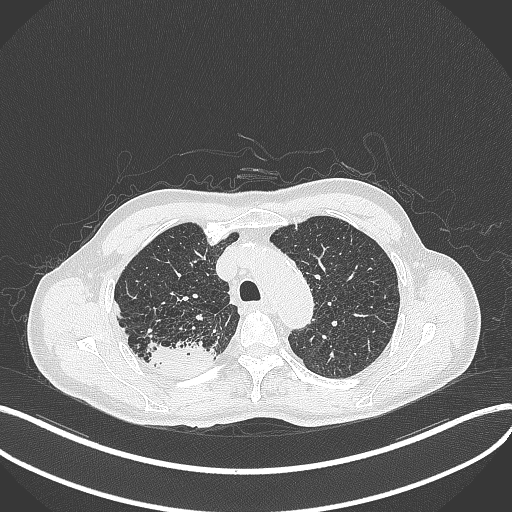
Chest CT, one axial slice. Position 340 of 428 along the scan axis. Reconstruction kernel B70f. 120 kVp. Lung window (W 1500 / L -600 HU). 1 mm slice thickness. 512 × 512 image matrix, field of view 400 × 400 mm. Patient: male, 79 years. From the clinical record (not read from this slice): clinical TNM (as recorded): T3 N0 M0.
Structures marked on this image (rectangle marked by the reading radiologist):
- lung tumour (recorded histology: adenocarcinoma): bounding box <148,339,219,379> (left, top, right, bottom; pixels)